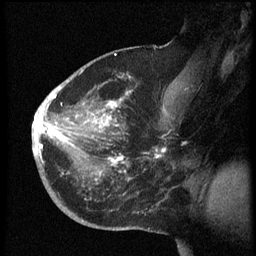
Breast MRI (dynamic contrast-enhanced), one sagittal slice. Slice 37 of 60 in the series (ordered by position). Dynamic contrast-enhanced series, image 2 of 3 at this slice position (ordered by acquisition). 1.5 T. TE 4.2 ms, TR 8.4 ms. 2.5 mm slice thickness. 256 × 256 image matrix, field of view 200 × 200 mm. Female patient, age 38 years. Case-level facts recorded for this patient, not image findings: setting: breast cancer imaged before/during neoadjuvant chemotherapy; receptor status: HER2-positive.
Annotated regions visible in this slice (semi-automatic segmentation, software-assisted and operator-edited):
- analysis volume of interest (the breast-tissue region the enhancement analysis was run in; not a lesion): bounding box <33,74,173,202> (left, top, right, bottom; pixels)
- tumour enhancement mask (voxels above the 70 % enhancement threshold inside the analysis volume of interest): <33,77,168,182>